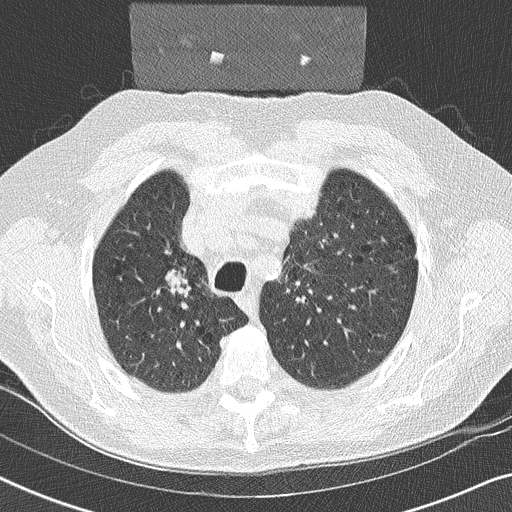
Chest CT (low-dose screening protocol), one axial image; second screening round (one year after baseline); lung window (W 1500 / L -600 HU); 2 mm slice thickness; 120 kVp; slice 68 of 252 in the series. Male participant, aged 59 years at enrolment. Former smoker at enrolment.
Lesion marked by an expert reader, bounding box [x1, y1, x2, y2] px = [154, 260, 208, 307]. The exam's reader record, not a measurement of the box and not confirmed to be the same lesion: non-calcified nodule or mass ≥4 mm, right upper lobe, 17 × 16 mm, smooth margins, soft tissue attenuation, pre-existing on the prior screen: yes.